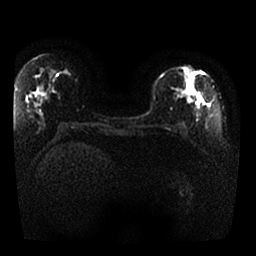
Breast MRI, one axial slice. Slice 14 of 25 in the series (ordered by position). Diffusion-weighted series; image 2 of 4 stored at this slice position (different b-values; order by instance number). 1.5 T. 256 × 256 image matrix. Female patient.
Annotated regions visible in this slice (manually delineated by an expert):
- tumour on diffusion-weighted imaging: bounding box [x1, y1, x2, y2] px = [170, 82, 194, 107]